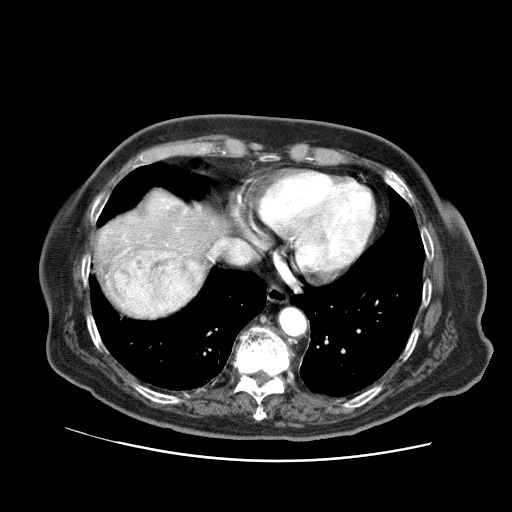
Contrast-enhanced abdominal CT (liver protocol), one axial slice; slice 61 of 73 in the series (ordered by position); reconstruction kernel STANDARD; soft-tissue window (W 400 / L 40 HU); 2.5 mm slice thickness; 512 × 512 image matrix. From the clinical record (not read from this slice): diagnosis: hepatocellular carcinoma (patient treated with transarterial chemoembolisation; whether this scan precedes or follows treatment is not stated here); TNM stage (as recorded): Stage-I; Child-Pugh class: A; tumour differentiation: well differentiated.
Annotated regions visible in this slice (semi-automatically segmented with operator editing):
- abdominal aorta: bounding box (x1, y1, x2, y2) in pixels: (281, 308, 306, 336)
- liver parenchyma outside the tumour (the mass and vessels are separate outlines, so this box may not span the whole liver): (94, 190, 230, 319)
- mass: (109, 251, 203, 319)
- liver vessels: (123, 199, 186, 253)